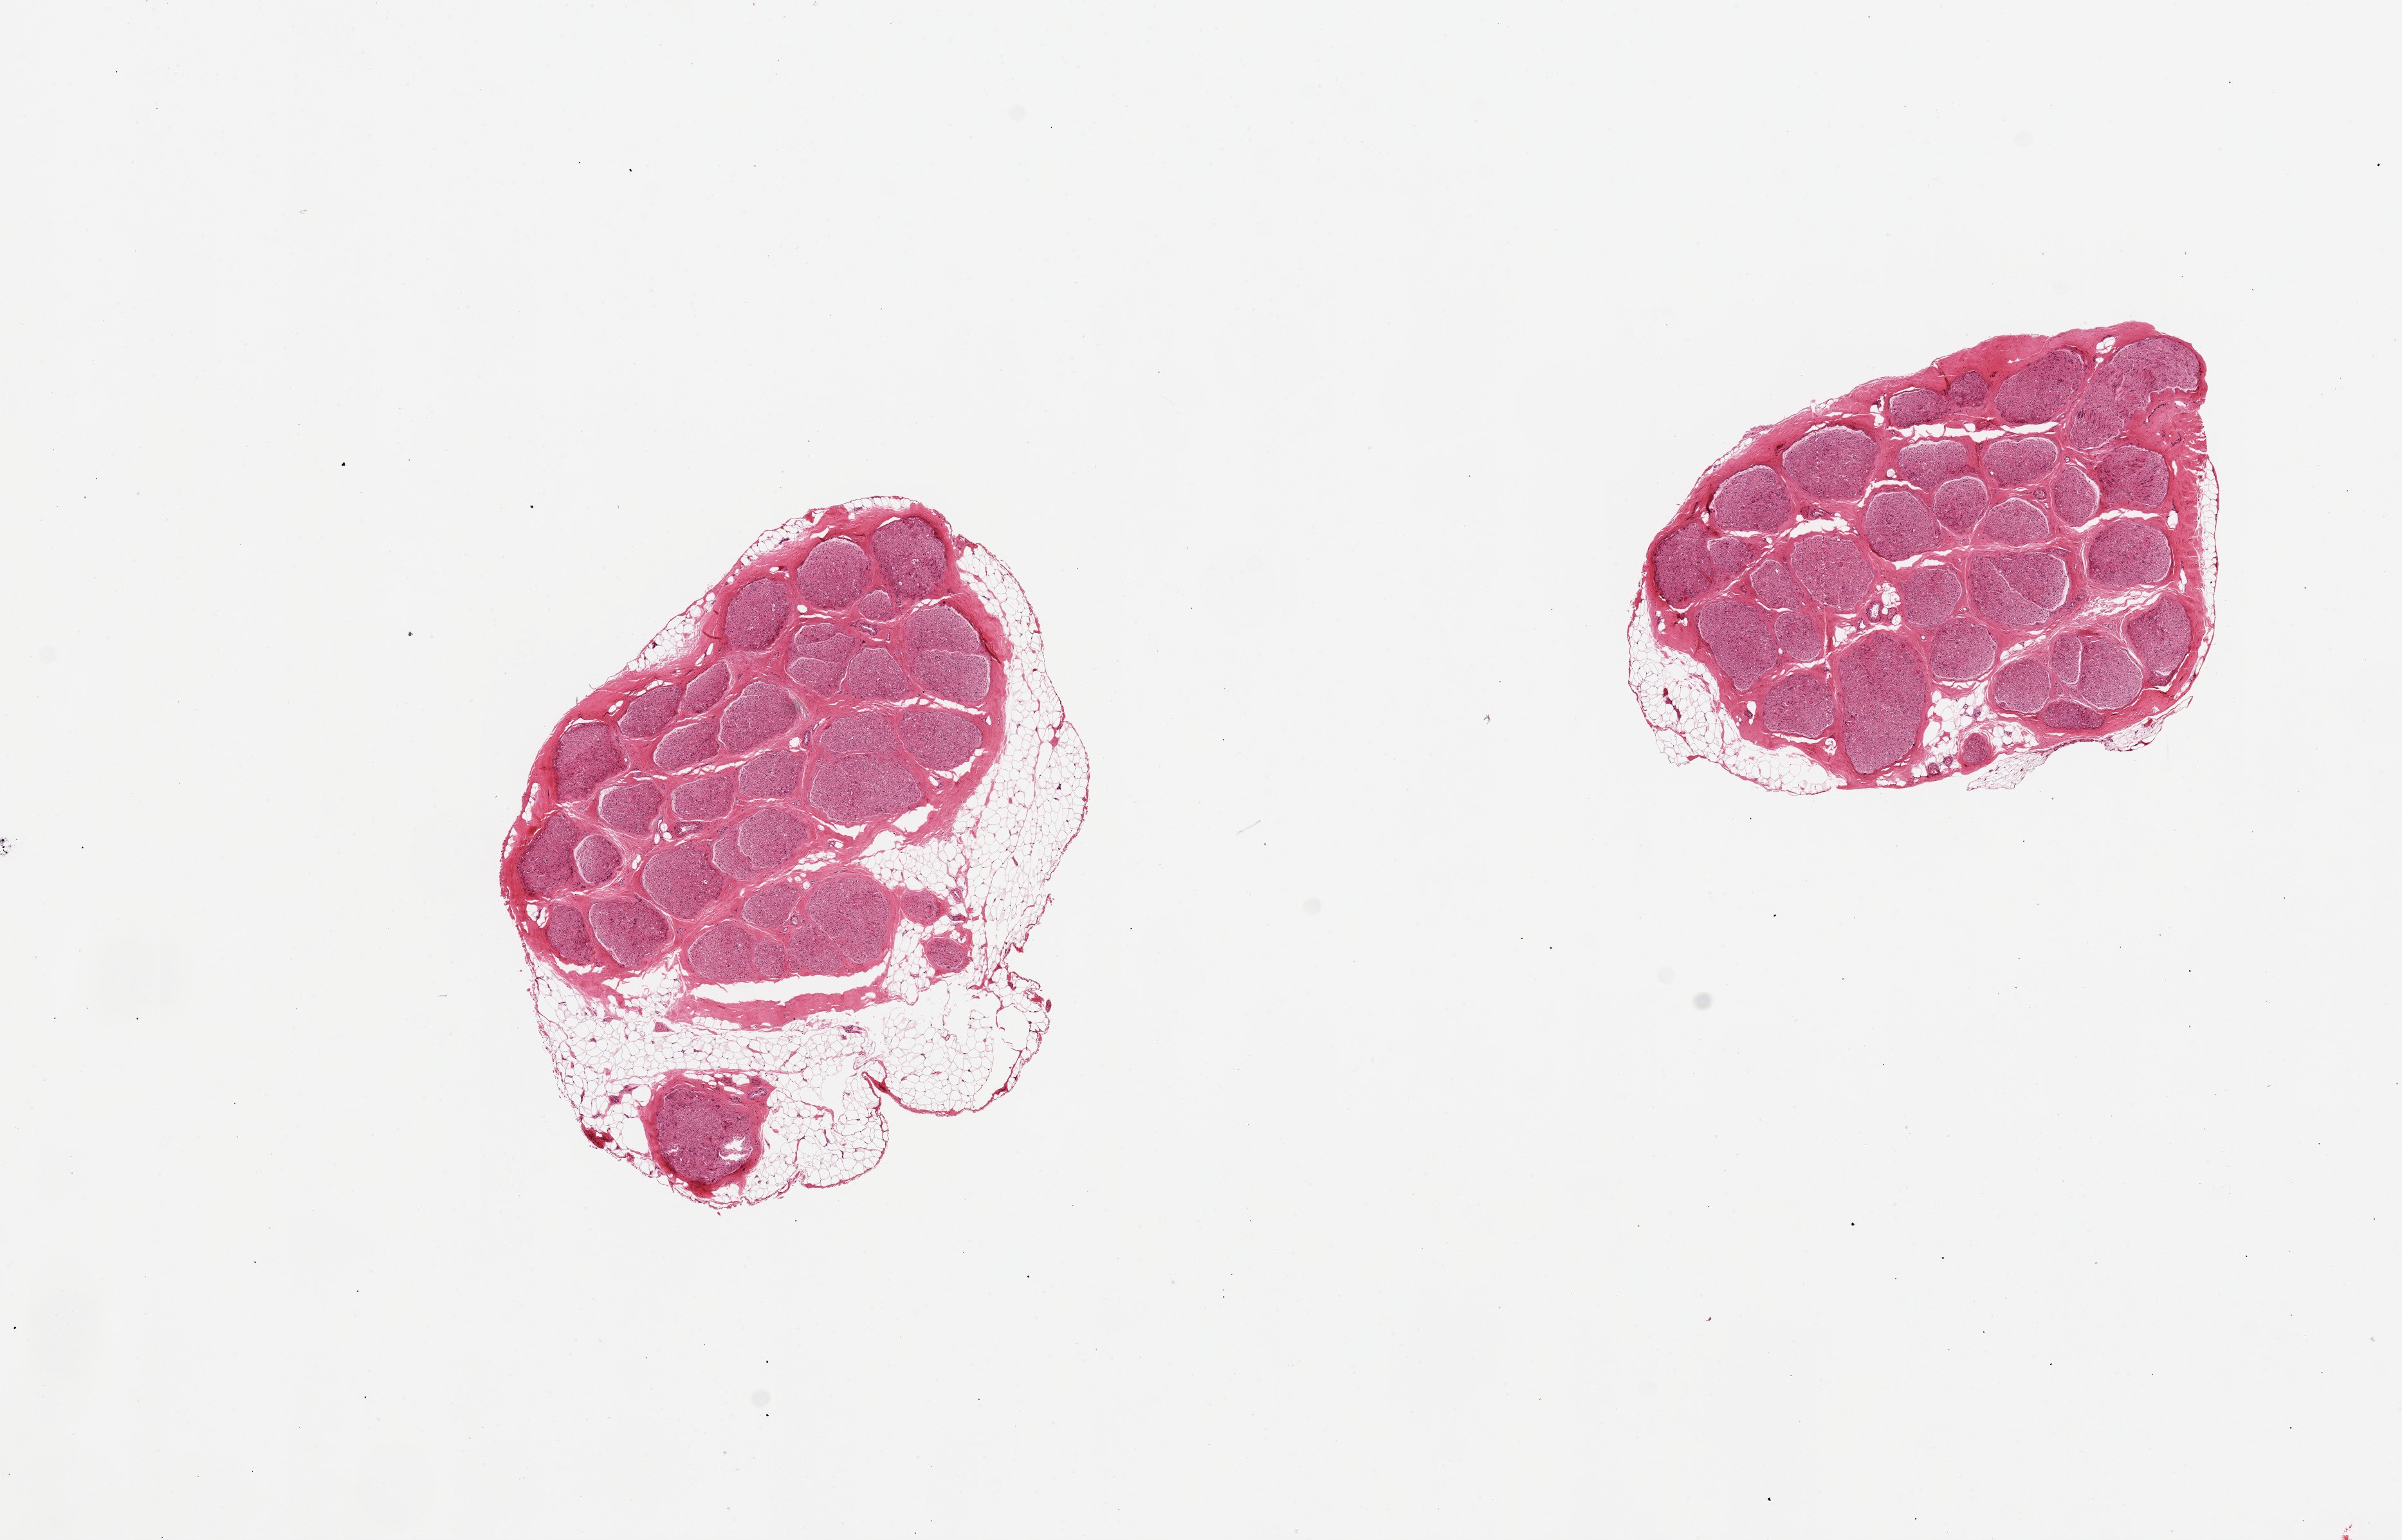
Whole-slide image, H&E stain, shown as a low-resolution overview of the whole scanned area (about 14.8 x 9.5 mm, from a 20x scan), PAXgene-fixed paraffin-embedded (PFPE) section, sampled site (target tissue): tibial nerve, tissue donor sample.
Pathologist's review note for this sample: 2 pieces; up to 1mm external fat on 1 piece comprising 40% of area.